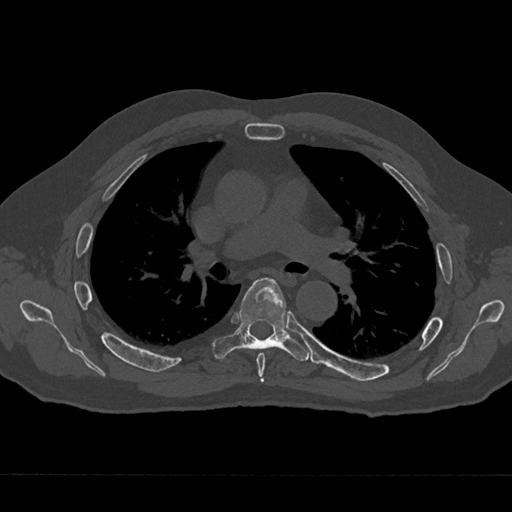
CT including the spine, one axial slice. Slice 438 of 797 in the series (ordered by position). 120 kVp. Bone window (W 1800 / L 400 HU). 512 × 512 image matrix. Male patient, age 75 years. Case-level facts recorded for this patient, not image findings: primary cancer: renal.
Outlined on this slice (semi-automatic segmentation, software-assisted and operator-edited):
- T5 vertebra: bounding box <256,353,266,382> (left, top, right, bottom; pixels)
- T6 vertebra: <213,277,310,361>